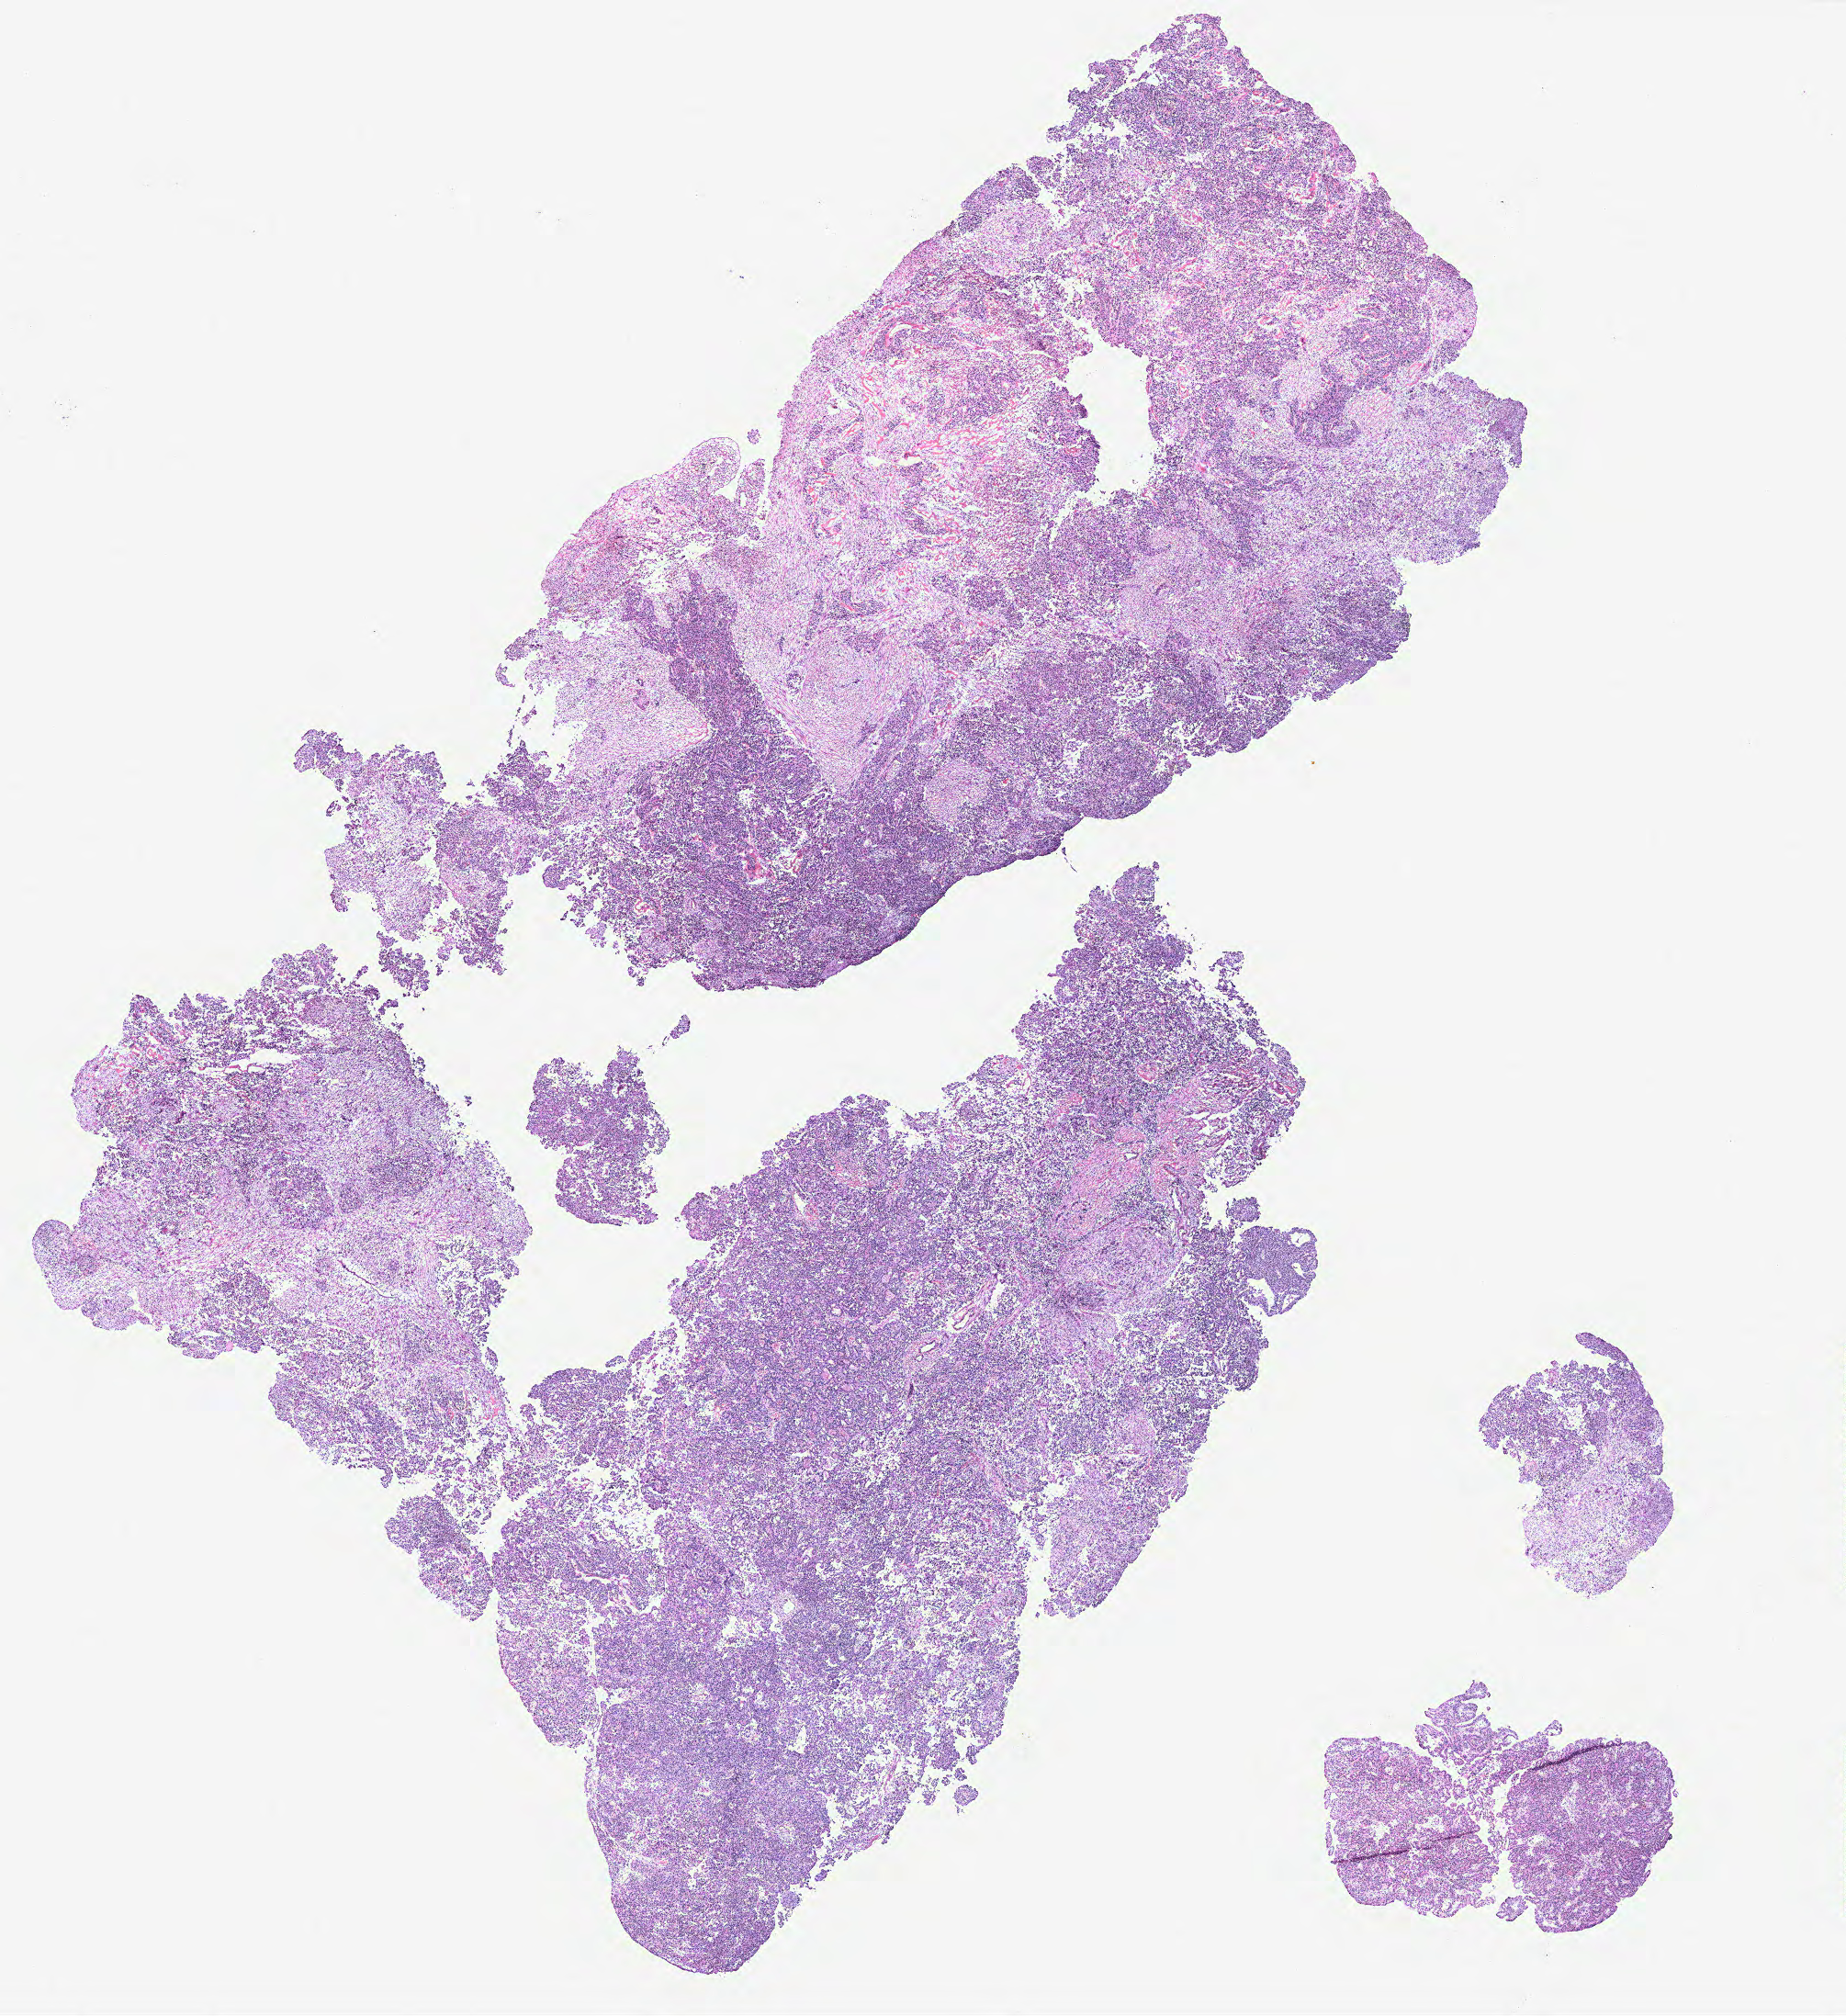
Digitized H&E tissue section (whole slide) — whole scanned area (about 16.1 x 17.6 mm, from a 40x scan) shown as a low-resolution overview, ovary, tumour tissue. 79-year-old female patient.
Primary tumour site (as recorded): ovary. Histologic diagnosis: Serous adenocarcinoma, NOS.